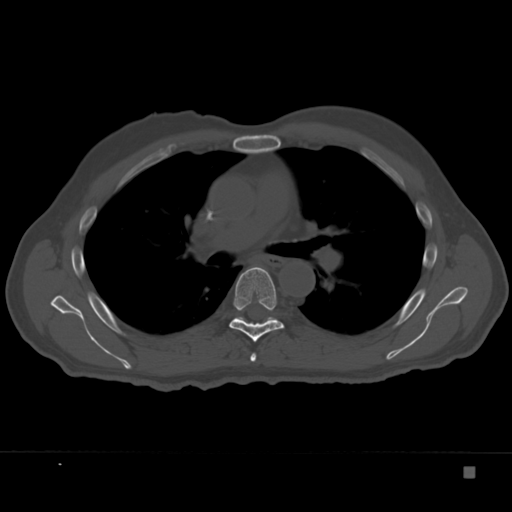
CT including the spine, one axial slice; slice 240 of 332 in the series (ordered by position); reconstruction kernel Br40s; bone window (W 1800 / L 400 HU); 512 × 512 image matrix, field of view 389 × 389 mm. Patient: male, 72 years. Case-level facts recorded for this patient, not image findings: primary cancer: skeletal.
Structures marked on this image (semi-automatically segmented with operator editing):
- T5 vertebra: bounding box <250,353,256,362> (left, top, right, bottom; pixels)
- T6 vertebra: <229,267,285,342>